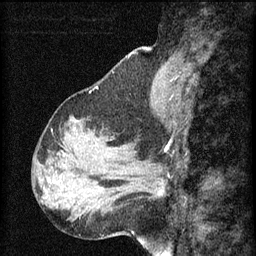
Breast MRI (dynamic contrast-enhanced), one sagittal slice. Slice 21 of 60 in the series (ordered by position). 3 images stored at this slice position (order not interpretable as contrast timing). 1.5 T. TE 4.2 ms, TR 8.2 ms. 2 mm slice thickness. 256 × 256 image matrix, field of view 180 × 180 mm. Patient: female, 37 years.
Outlined on this slice (semi-automatic segmentation, software-assisted and operator-edited):
- analysis volume of interest (the breast-tissue region the enhancement analysis was run in; not a lesion): bounding box (x1, y1, x2, y2) in pixels: (126, 156, 166, 205)
- tumour enhancement mask (voxels above the 70 % enhancement threshold inside the analysis volume of interest): (157, 182, 164, 195)